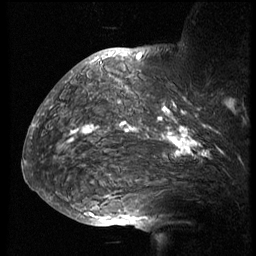
Breast MRI (dynamic contrast-enhanced), one sagittal slice; slice 49 of 74 in the series (ordered by position); 3 images stored at this slice position (order not interpretable as contrast timing); 1.5 T; TE 4.2 ms, TR 8.9 ms; 2.5 mm slice thickness; 256 × 256 image matrix. Patient: female, 57 years. Case-level facts recorded for this patient, not image findings: setting: breast cancer imaged before/during neoadjuvant chemotherapy; receptor status: HER2-positive.
Outlined on this slice (semi-automatic segmentation, software-assisted and operator-edited):
- analysis volume of interest (the breast-tissue region the enhancement analysis was run in; not a lesion): bounding box (x1, y1, x2, y2) in pixels: (51, 67, 246, 173)
- tumour enhancement mask (voxels above the 140 % enhancement threshold inside the analysis volume of interest): (70, 108, 236, 156)